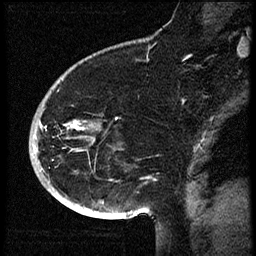
Breast MRI (dynamic contrast-enhanced), one sagittal slice; position 41 of 60 along the scan axis; dynamic contrast-enhanced study with each time point stored as its own series, time point 2 of 3 at this slice position (early post-contrast, ordered by acquisition time); 1.5 T; TE 4.2 ms, TR 18.9 ms; 256 × 256 image matrix, field of view 200 × 200 mm. Female patient. Case-level facts recorded for this patient, not image findings: setting: breast cancer imaged before/during neoadjuvant chemotherapy; receptor status: HR-positive, HER2-negative.
Outlined on this slice (semi-automatic segmentation, software-assisted and operator-edited):
- analysis volume of interest (the breast-tissue region the enhancement analysis was run in; not a lesion): box from (x=32, y=87) to (x=110, y=173) px
- tumour enhancement mask (voxels above the 100 % enhancement threshold inside the analysis volume of interest): (x=33, y=121)–(x=77, y=148)